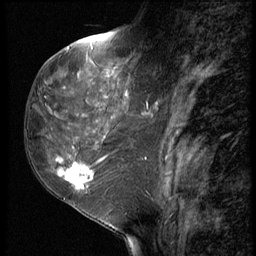
Breast MRI (dynamic contrast-enhanced), one sagittal slice; slice 27 of 62 in the series (ordered by position); 3 images stored at this slice position (order not interpretable as contrast timing); 1.5 T; TE 4.2 ms, TR 9 ms; 2.5 mm slice thickness; 256 × 256 image matrix. Female patient, age 50 years. Case-level facts recorded for this patient, not image findings: setting: breast cancer imaged before/during neoadjuvant chemotherapy; receptor status: HR-positive, HER2-negative.
Structures marked on this image (semi-automatically segmented with operator editing):
- analysis volume of interest (the breast-tissue region the enhancement analysis was run in; not a lesion): box from (x=32, y=91) to (x=118, y=209) px
- tumour enhancement mask (voxels above the 140 % enhancement threshold inside the analysis volume of interest): (x=58, y=156)–(x=108, y=189)